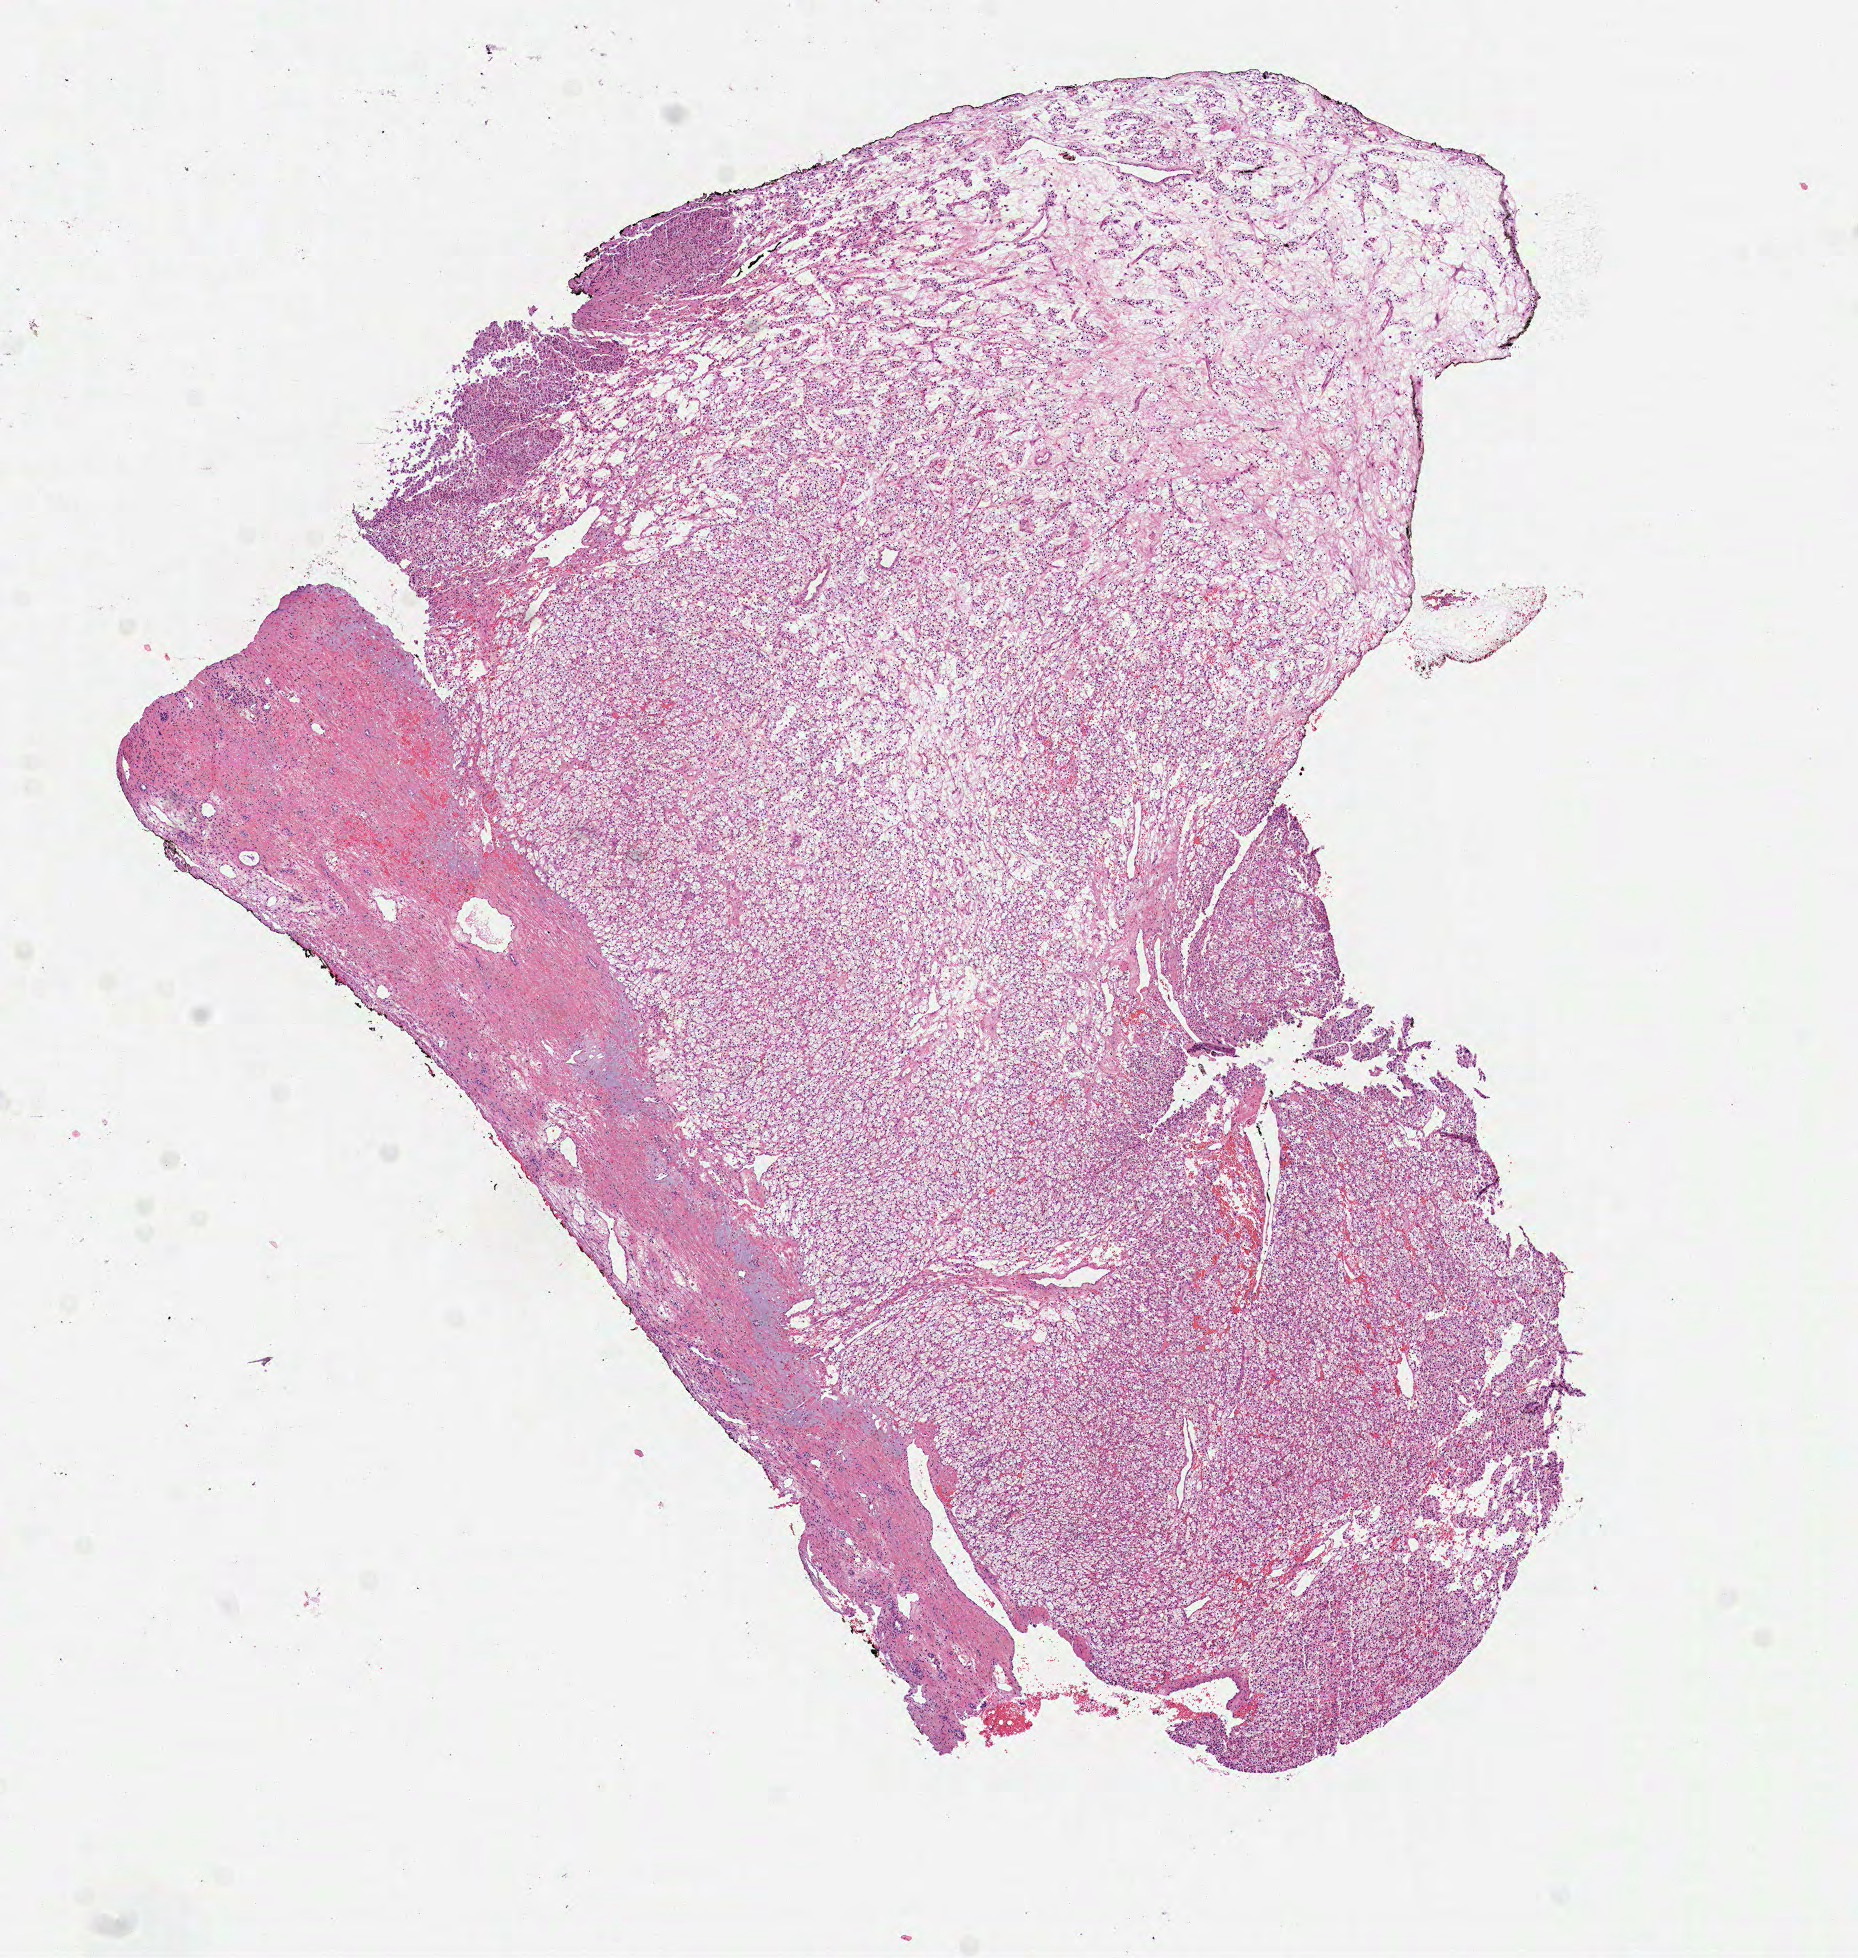
H&E whole-slide image, shown as a low-resolution overview of the whole scanned area (about 7.5 x 7.9 mm); formalin-fixed paraffin-embedded (FFPE) diagnostic section; kidney, primary tumour sample. Female, age 46 years at initial diagnosis. Histologic grade: G2 (moderately differentiated).
AJCC pathologic stage: I. Diagnosis: Clear cell adenocarcinoma, NOS. Laterality: left.